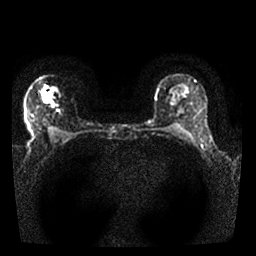
Breast MRI, one axial slice; position 19 of 25 along the scan axis; diffusion-weighted series; image 2 of 4 stored at this slice position (different b-values; order by instance number); 1.5 T; 256 × 256 image matrix, field of view 310 × 310 mm. Female patient.
Outlined on this slice (expert manual segmentation):
- tumour on diffusion-weighted imaging: box from (x=39, y=85) to (x=53, y=97) px